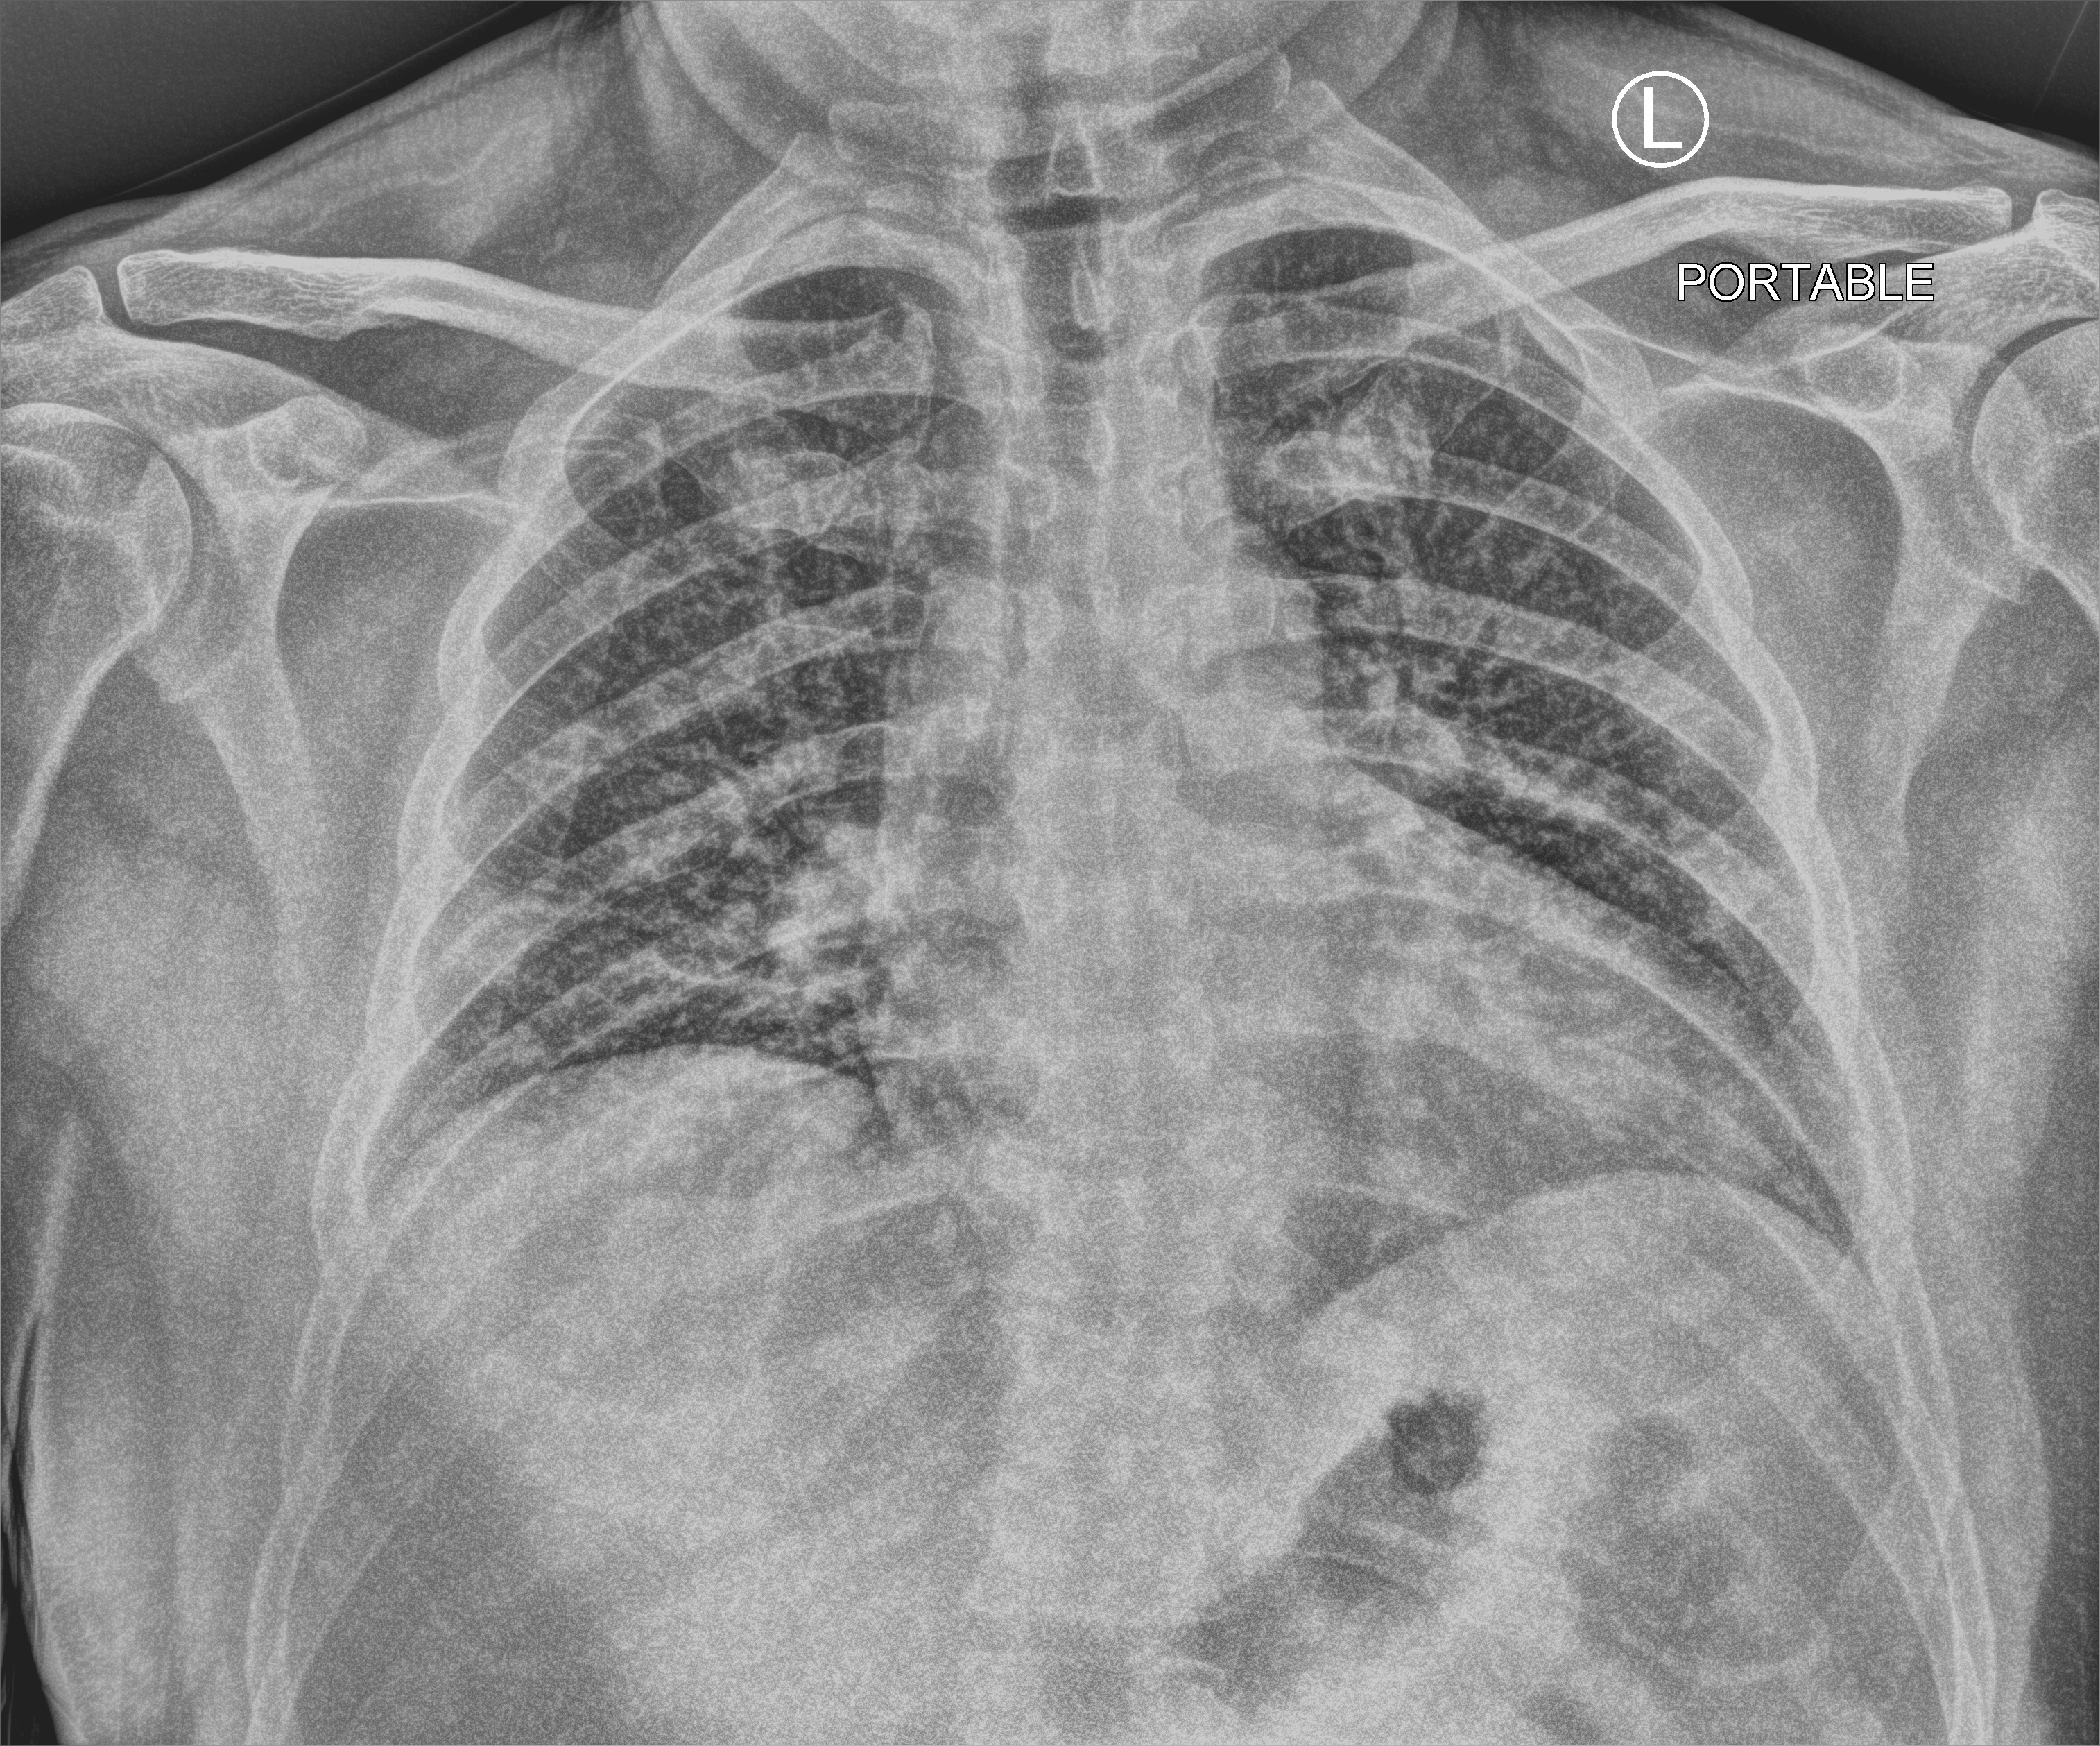
Portable chest radiograph, anteroposterior (AP) projection. Patient hospitalised with COVID-19; male, aged 18–59 years.
Hospital-stay facts (about this admission, not read from this image; timing relative to this image not recorded): length of hospital stay: 32 days.